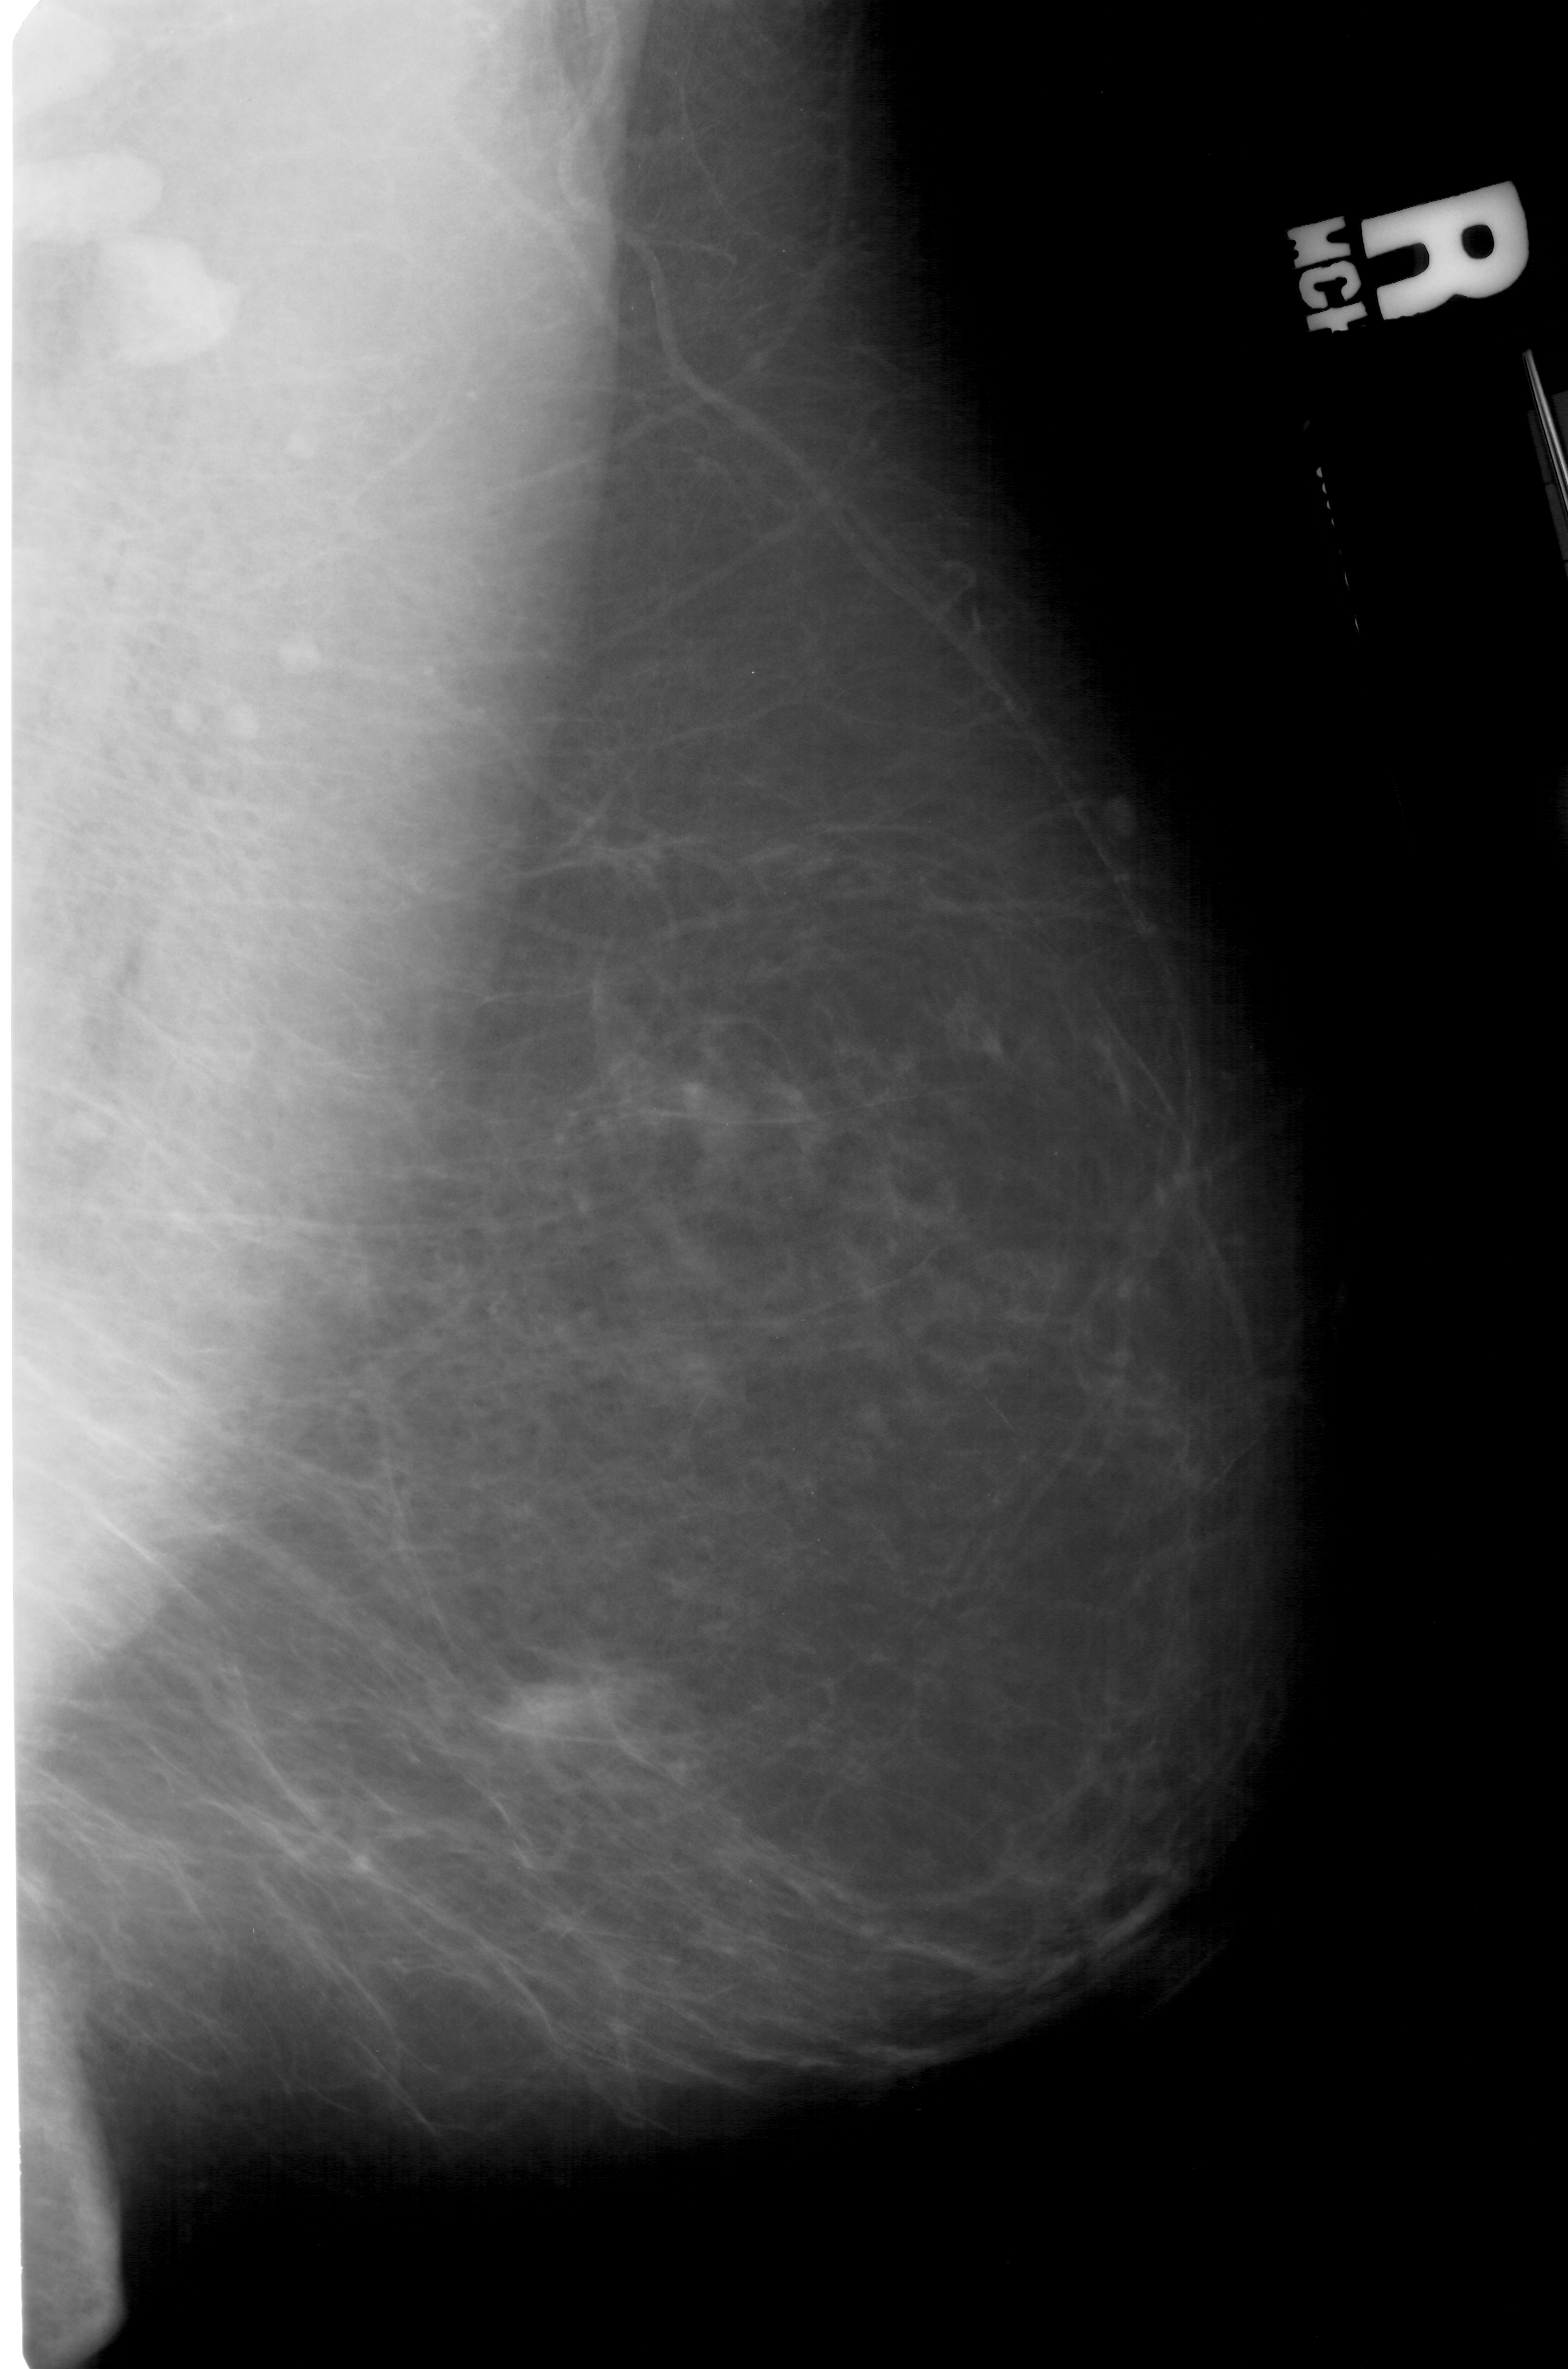
Digitized screen-film mammogram; right breast; MLO view; BI-RADS breast density category 2 (scale 1–4).
Radiologist-marked abnormalities on this image: mass, shape focal asymmetric density, margins ill defined; BI-RADS assessment category 4; subtlety rating 2 on a 1 (subtle) to 5 (obvious) scale; pathology result (as recorded, not read from the image): malignant.